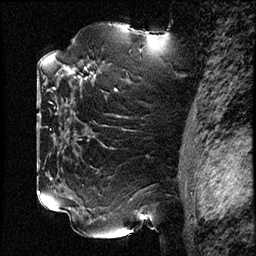
Breast MRI (dynamic contrast-enhanced), one sagittal slice. Slice 51 of 78 in the series (ordered by position). Dynamic contrast-enhanced study with each time point stored as its own series, time point 2 of 3 at this slice position (early post-contrast, ordered by acquisition time). 1.5 T. TE 4.2 ms, TR 17.6 ms. 2 mm slice thickness. 256 × 256 image matrix, field of view 200 × 200 mm. Patient: female, 42 years. From the clinical record (not read from this slice): setting: breast cancer imaged before/during neoadjuvant chemotherapy; receptor status: HER2-positive.
Structures marked on this image (semi-automatically segmented with operator editing):
- analysis volume of interest (the breast-tissue region the enhancement analysis was run in; not a lesion): bounding box [x1, y1, x2, y2] px = [50, 48, 130, 129]
- tumour enhancement mask (voxels above the 100 % enhancement threshold inside the analysis volume of interest): [64, 65, 87, 79]